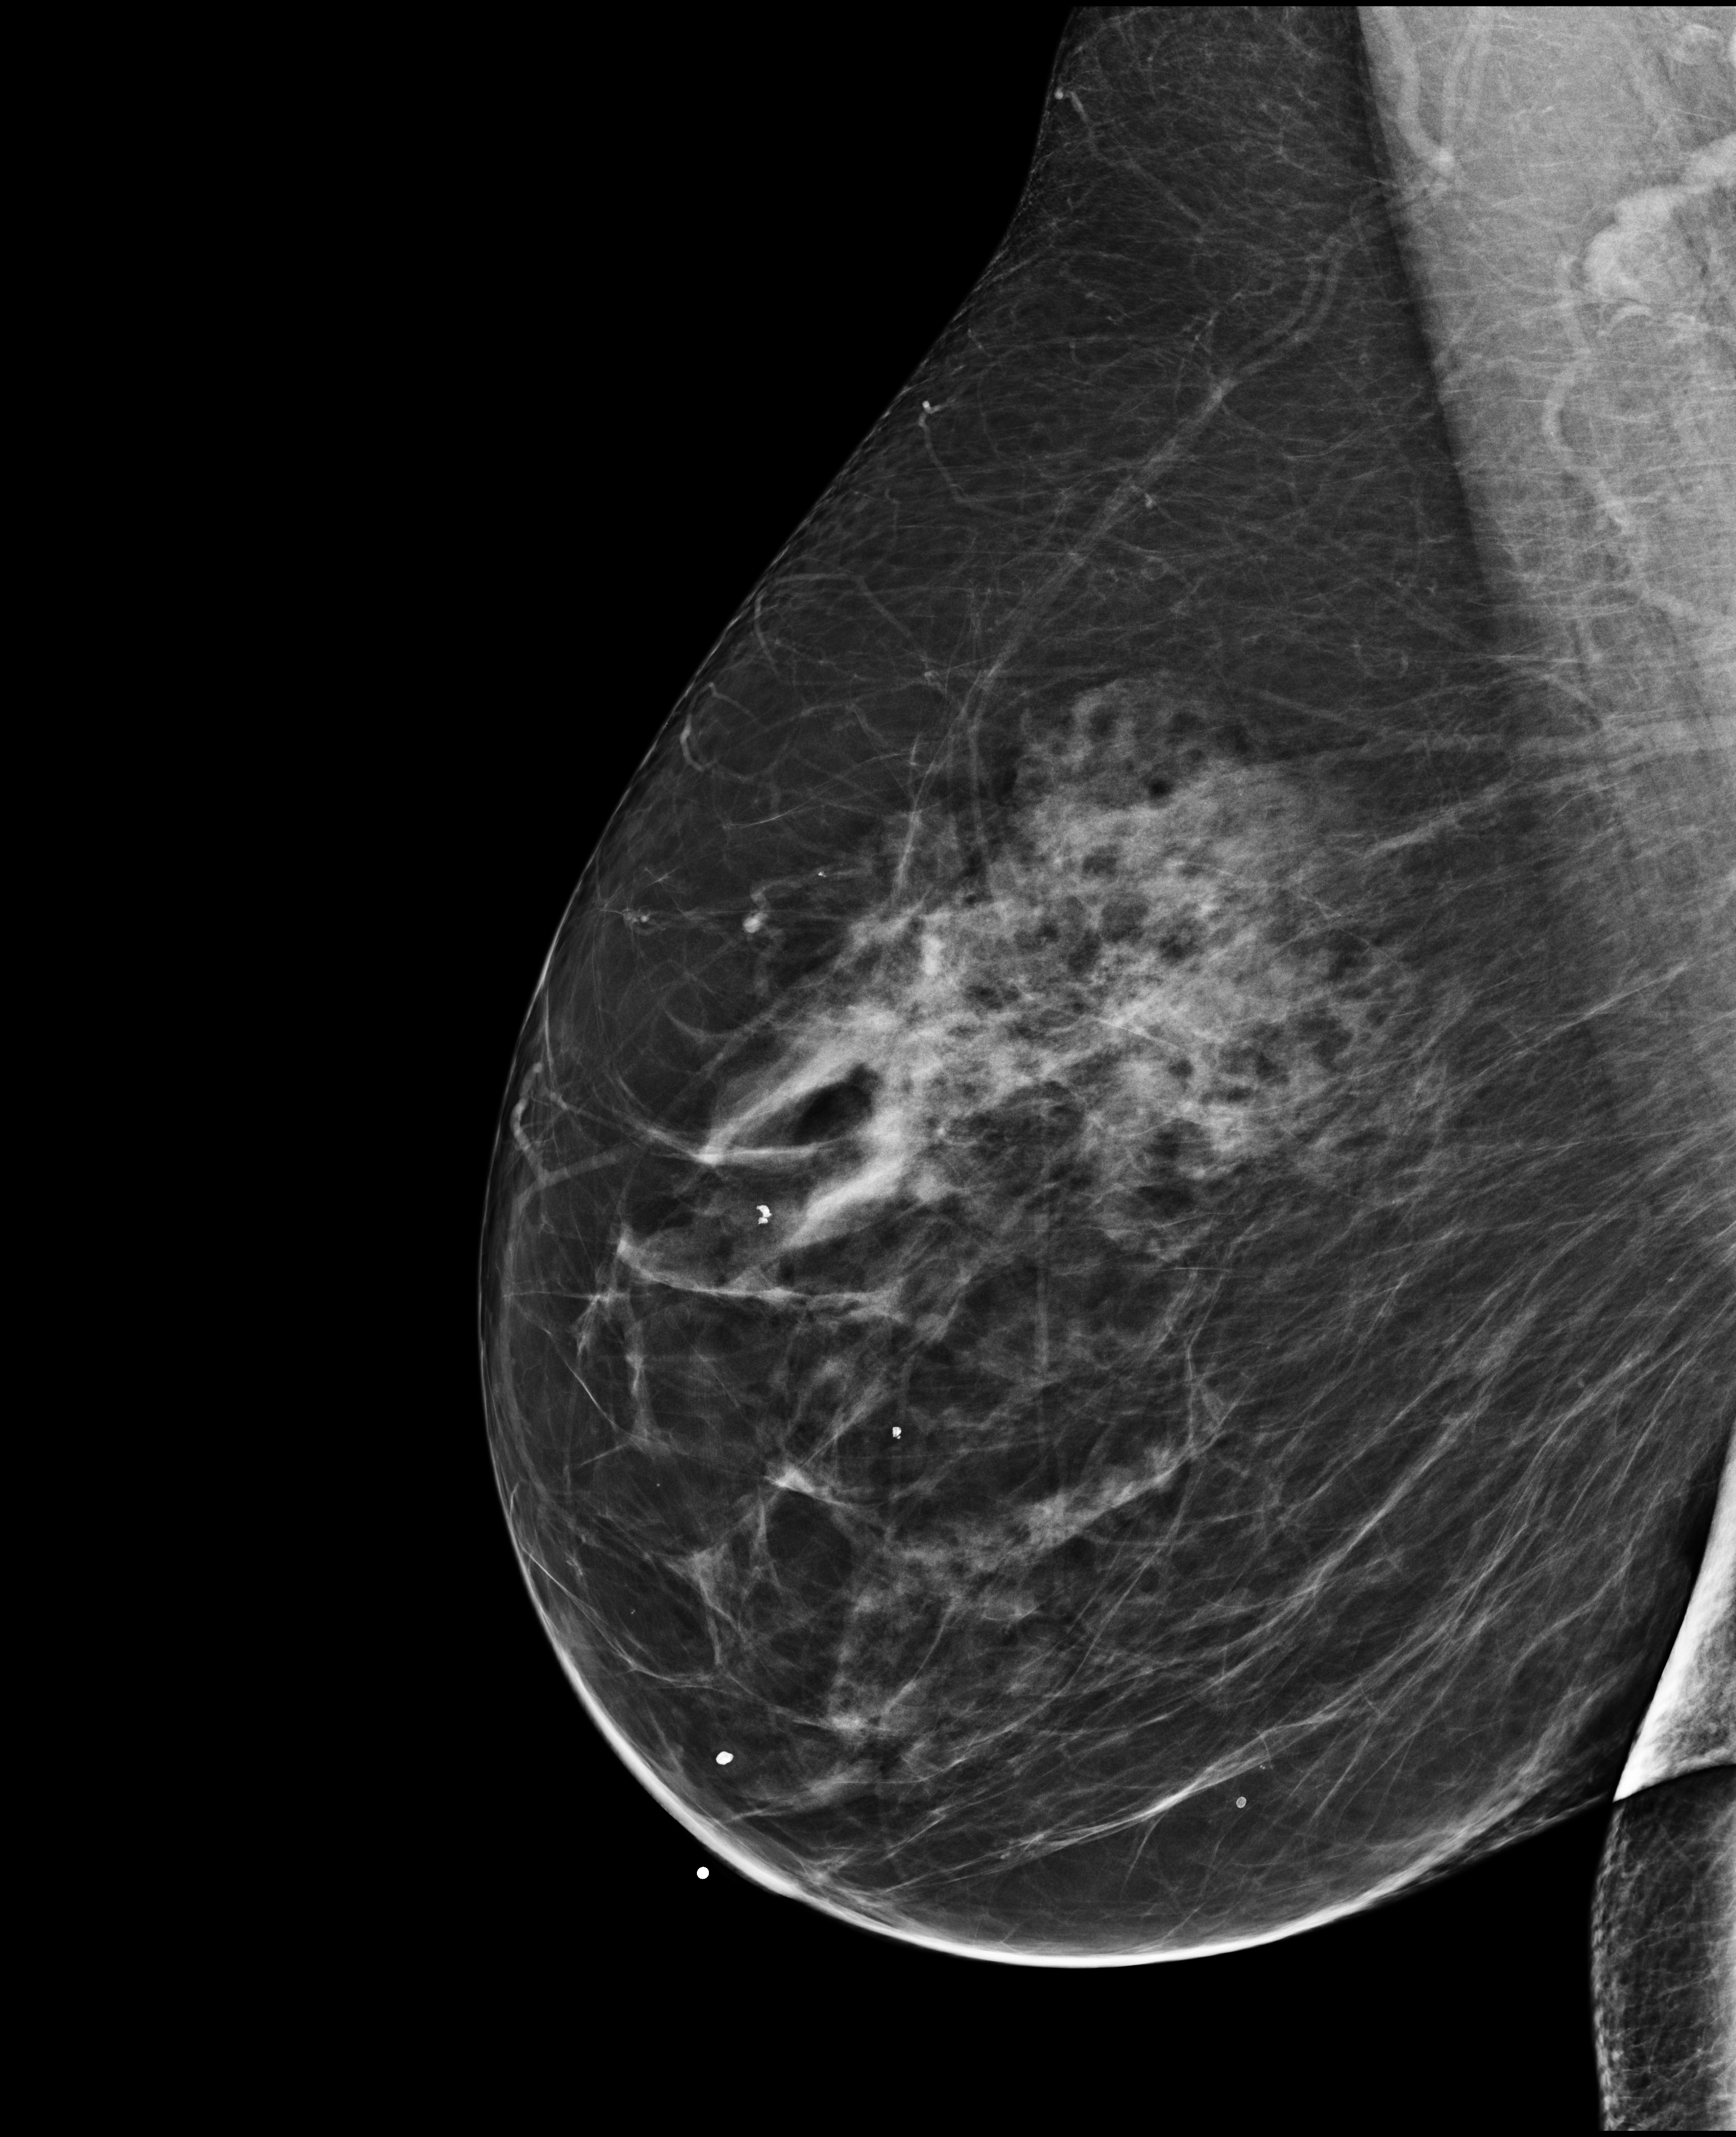
Annual screening mammography examination. Patient aged 61 years (female).
Image type: full-field digital mammogram. Breast: right. Projection: medio-lateral oblique projection.